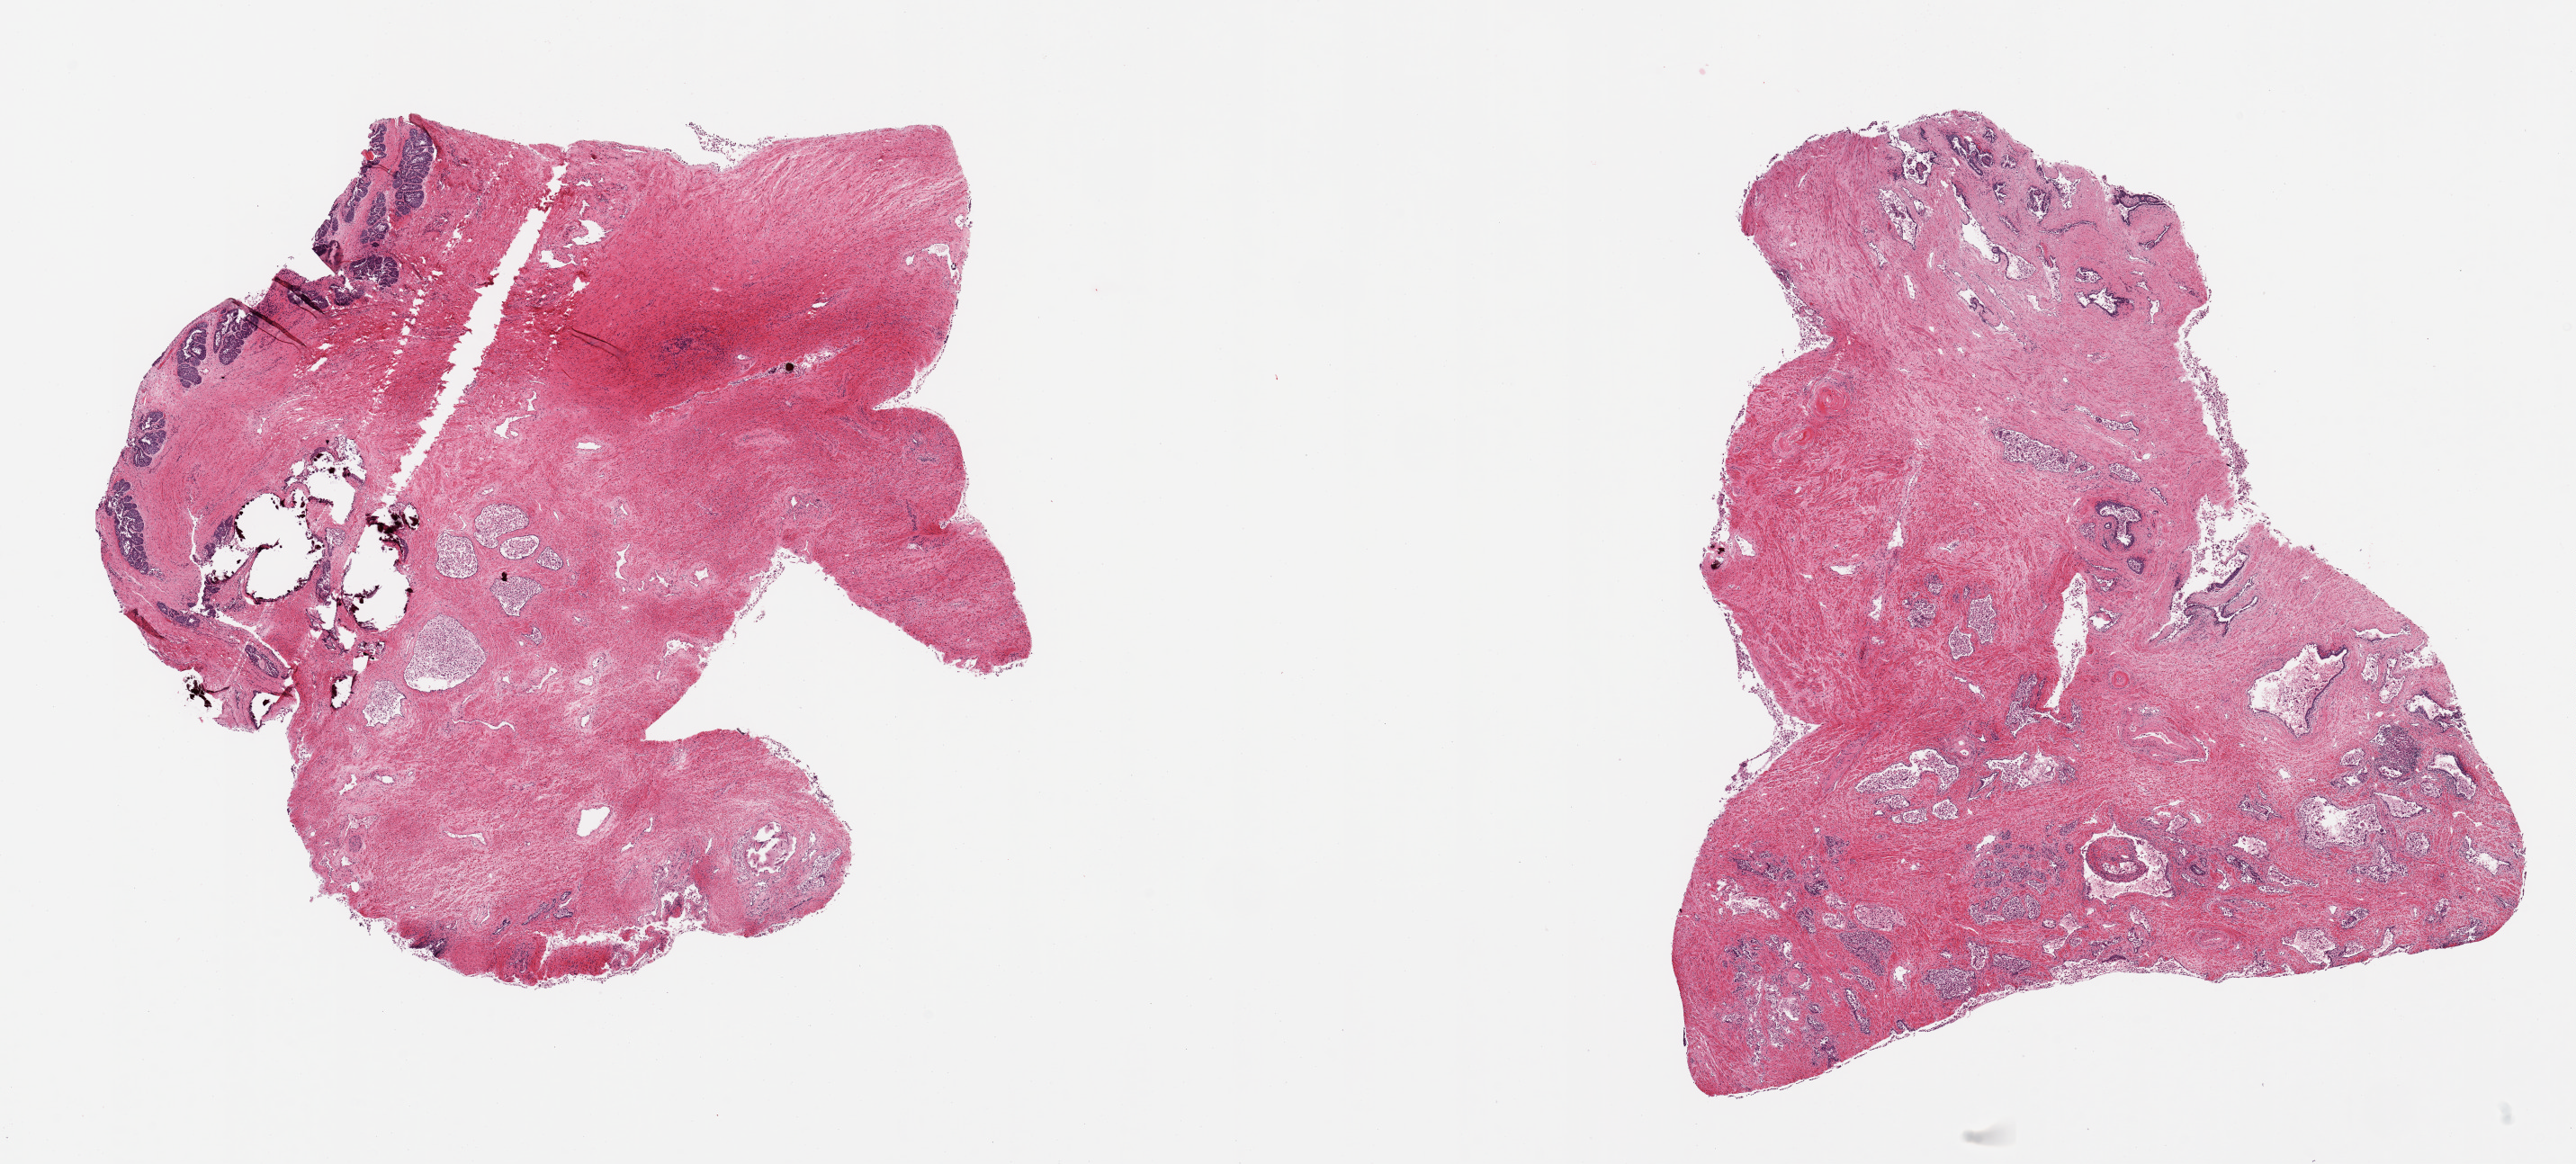
Whole-slide image, hematoxylin and eosin (H&E) stain, brightfield, a low-resolution overview of the entire scanned area, about 22.6 x 10.2 mm (slide scanned at 20x). PAXgene-fixed paraffin-embedded (PFPE) section. Target tissue: prostate. Donor tissue sample. Donor sex: male.
- reviewer comment on this tissue sample: 2 pieces; fibromuscular stroma and autolyzed prostatic glands; at one edge urothelium